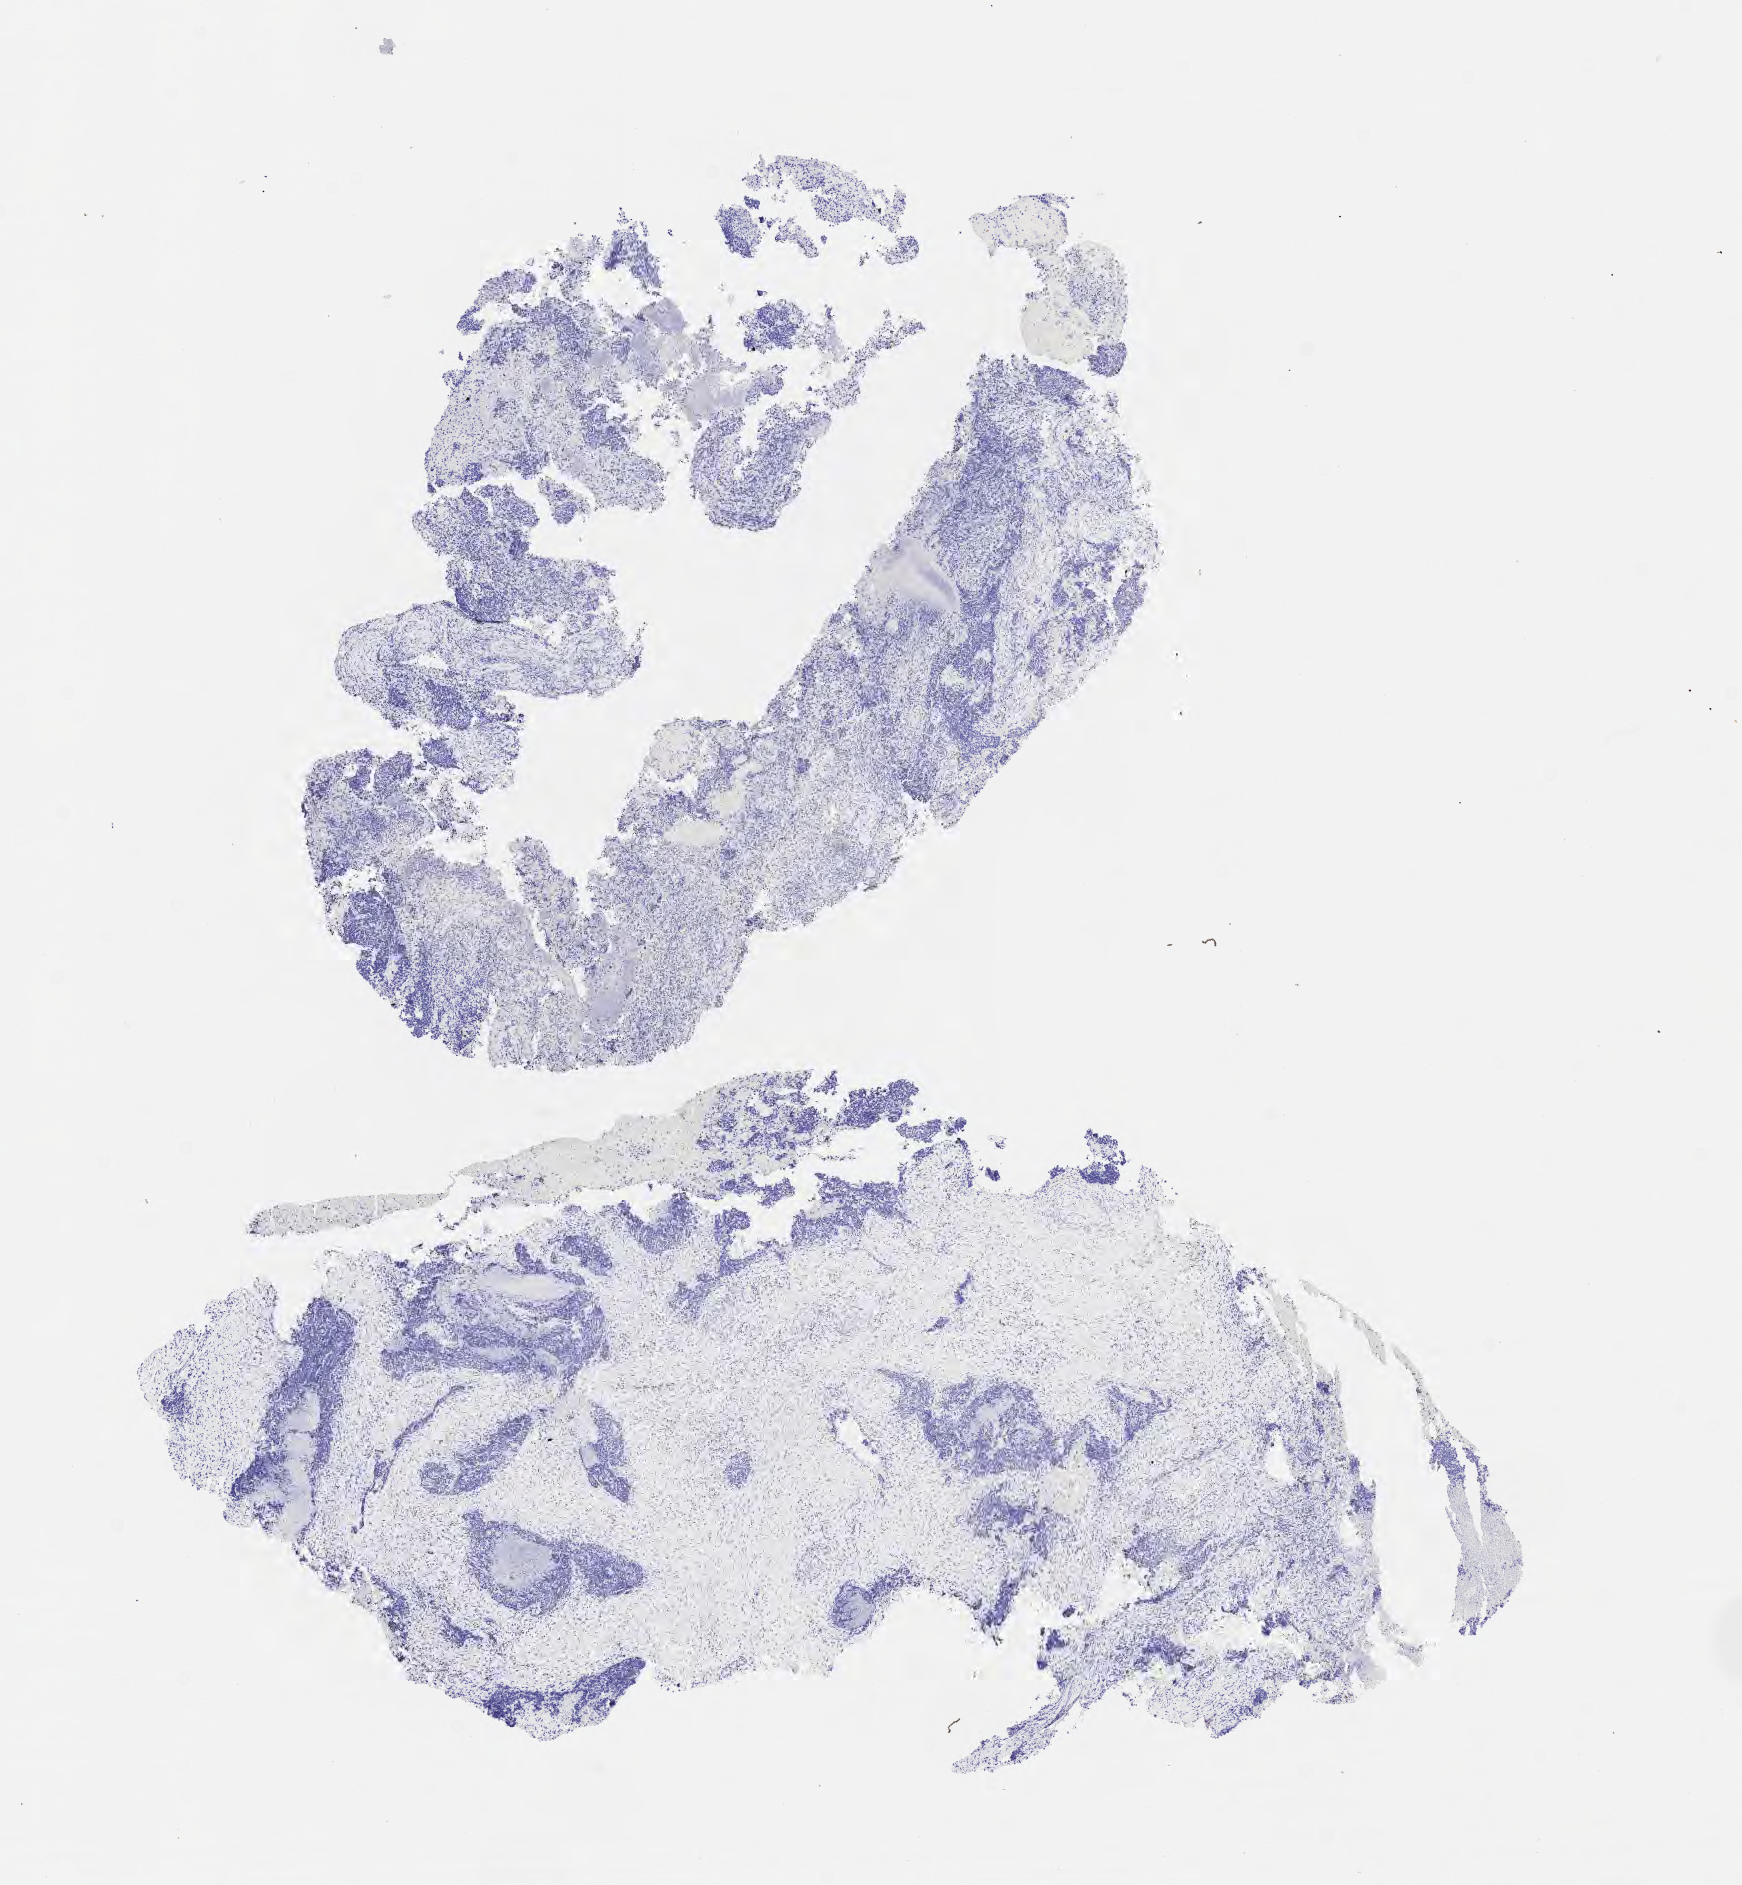
Whole-slide image, immunohistochemical stain for p63, a low-resolution overview of the entire scanned area, about 7.0 x 7.6 mm; specimen: tumor tissue; site: cervix. Female patient, 47 years old.
Histologic diagnosis: Squamous cell carcinoma, large cell, nonkeratinizing, NOS.